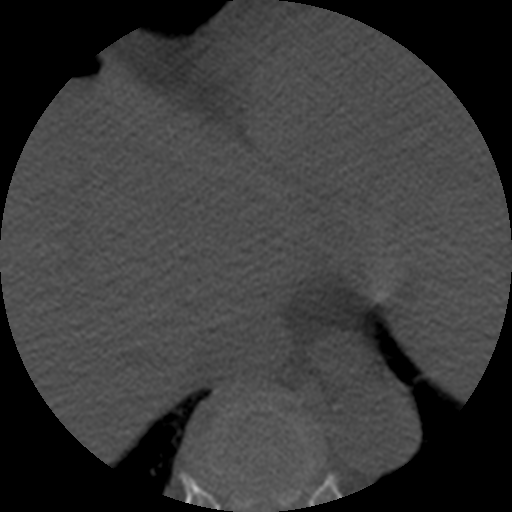
CT including the spine, one axial slice. Position 299 of 508 along the scan axis. Bone window (W 1800 / L 400 HU). 1.25 mm slice thickness. 512 × 512 image matrix, field of view 160 × 160 mm. Patient age 57 years. From the clinical record (not read from this slice): primary cancer: prostate.
Outlined on this slice (semi-automatic segmentation, software-assisted and operator-edited):
- T9 vertebra: box from (x=200, y=398) to (x=315, y=512) px